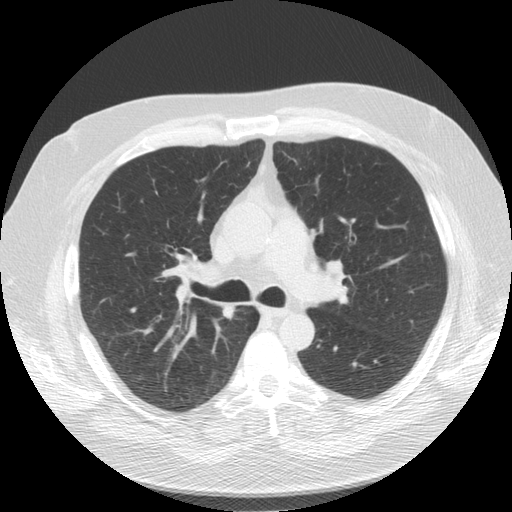
Low-dose screening chest CT, one axial slice; slice 91 of 136 in the series (ordered by position); reconstruction kernel STANDARD; 120 kVp; lung window (W 1500 / L -600 HU); 512 × 512 image matrix.
Structures marked on this image (manually delineated by an expert):
- lesion 1 (tumor, upper lobe of right lung): bounding box (x1, y1, x2, y2) in pixels: (222, 306, 236, 319)